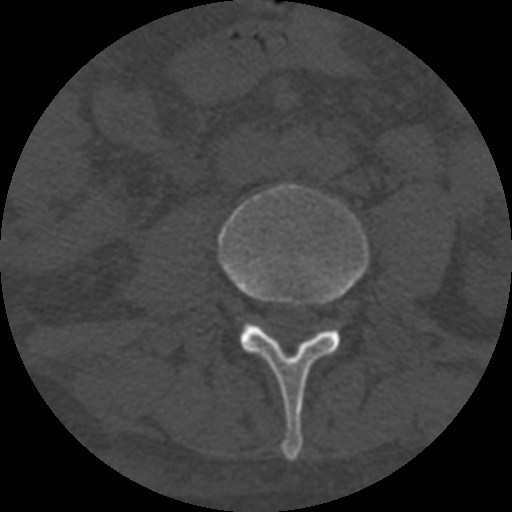
CT including the spine, one axial slice; slice 228 of 708 in the series (ordered by position); reconstruction kernel STANDARD; 120 kVp; one of 3 acquisitions stored at this slice position; bone window (W 1800 / L 400 HU); 1.25 mm slice thickness; 512 × 512 image matrix, field of view 160 × 160 mm. Patient age 55 years. From the clinical record (not read from this slice): primary cancer: colon.
Structures marked on this image (semi-automatically segmented with operator editing):
- L3 vertebra: box from (x=218, y=184) to (x=369, y=461) px